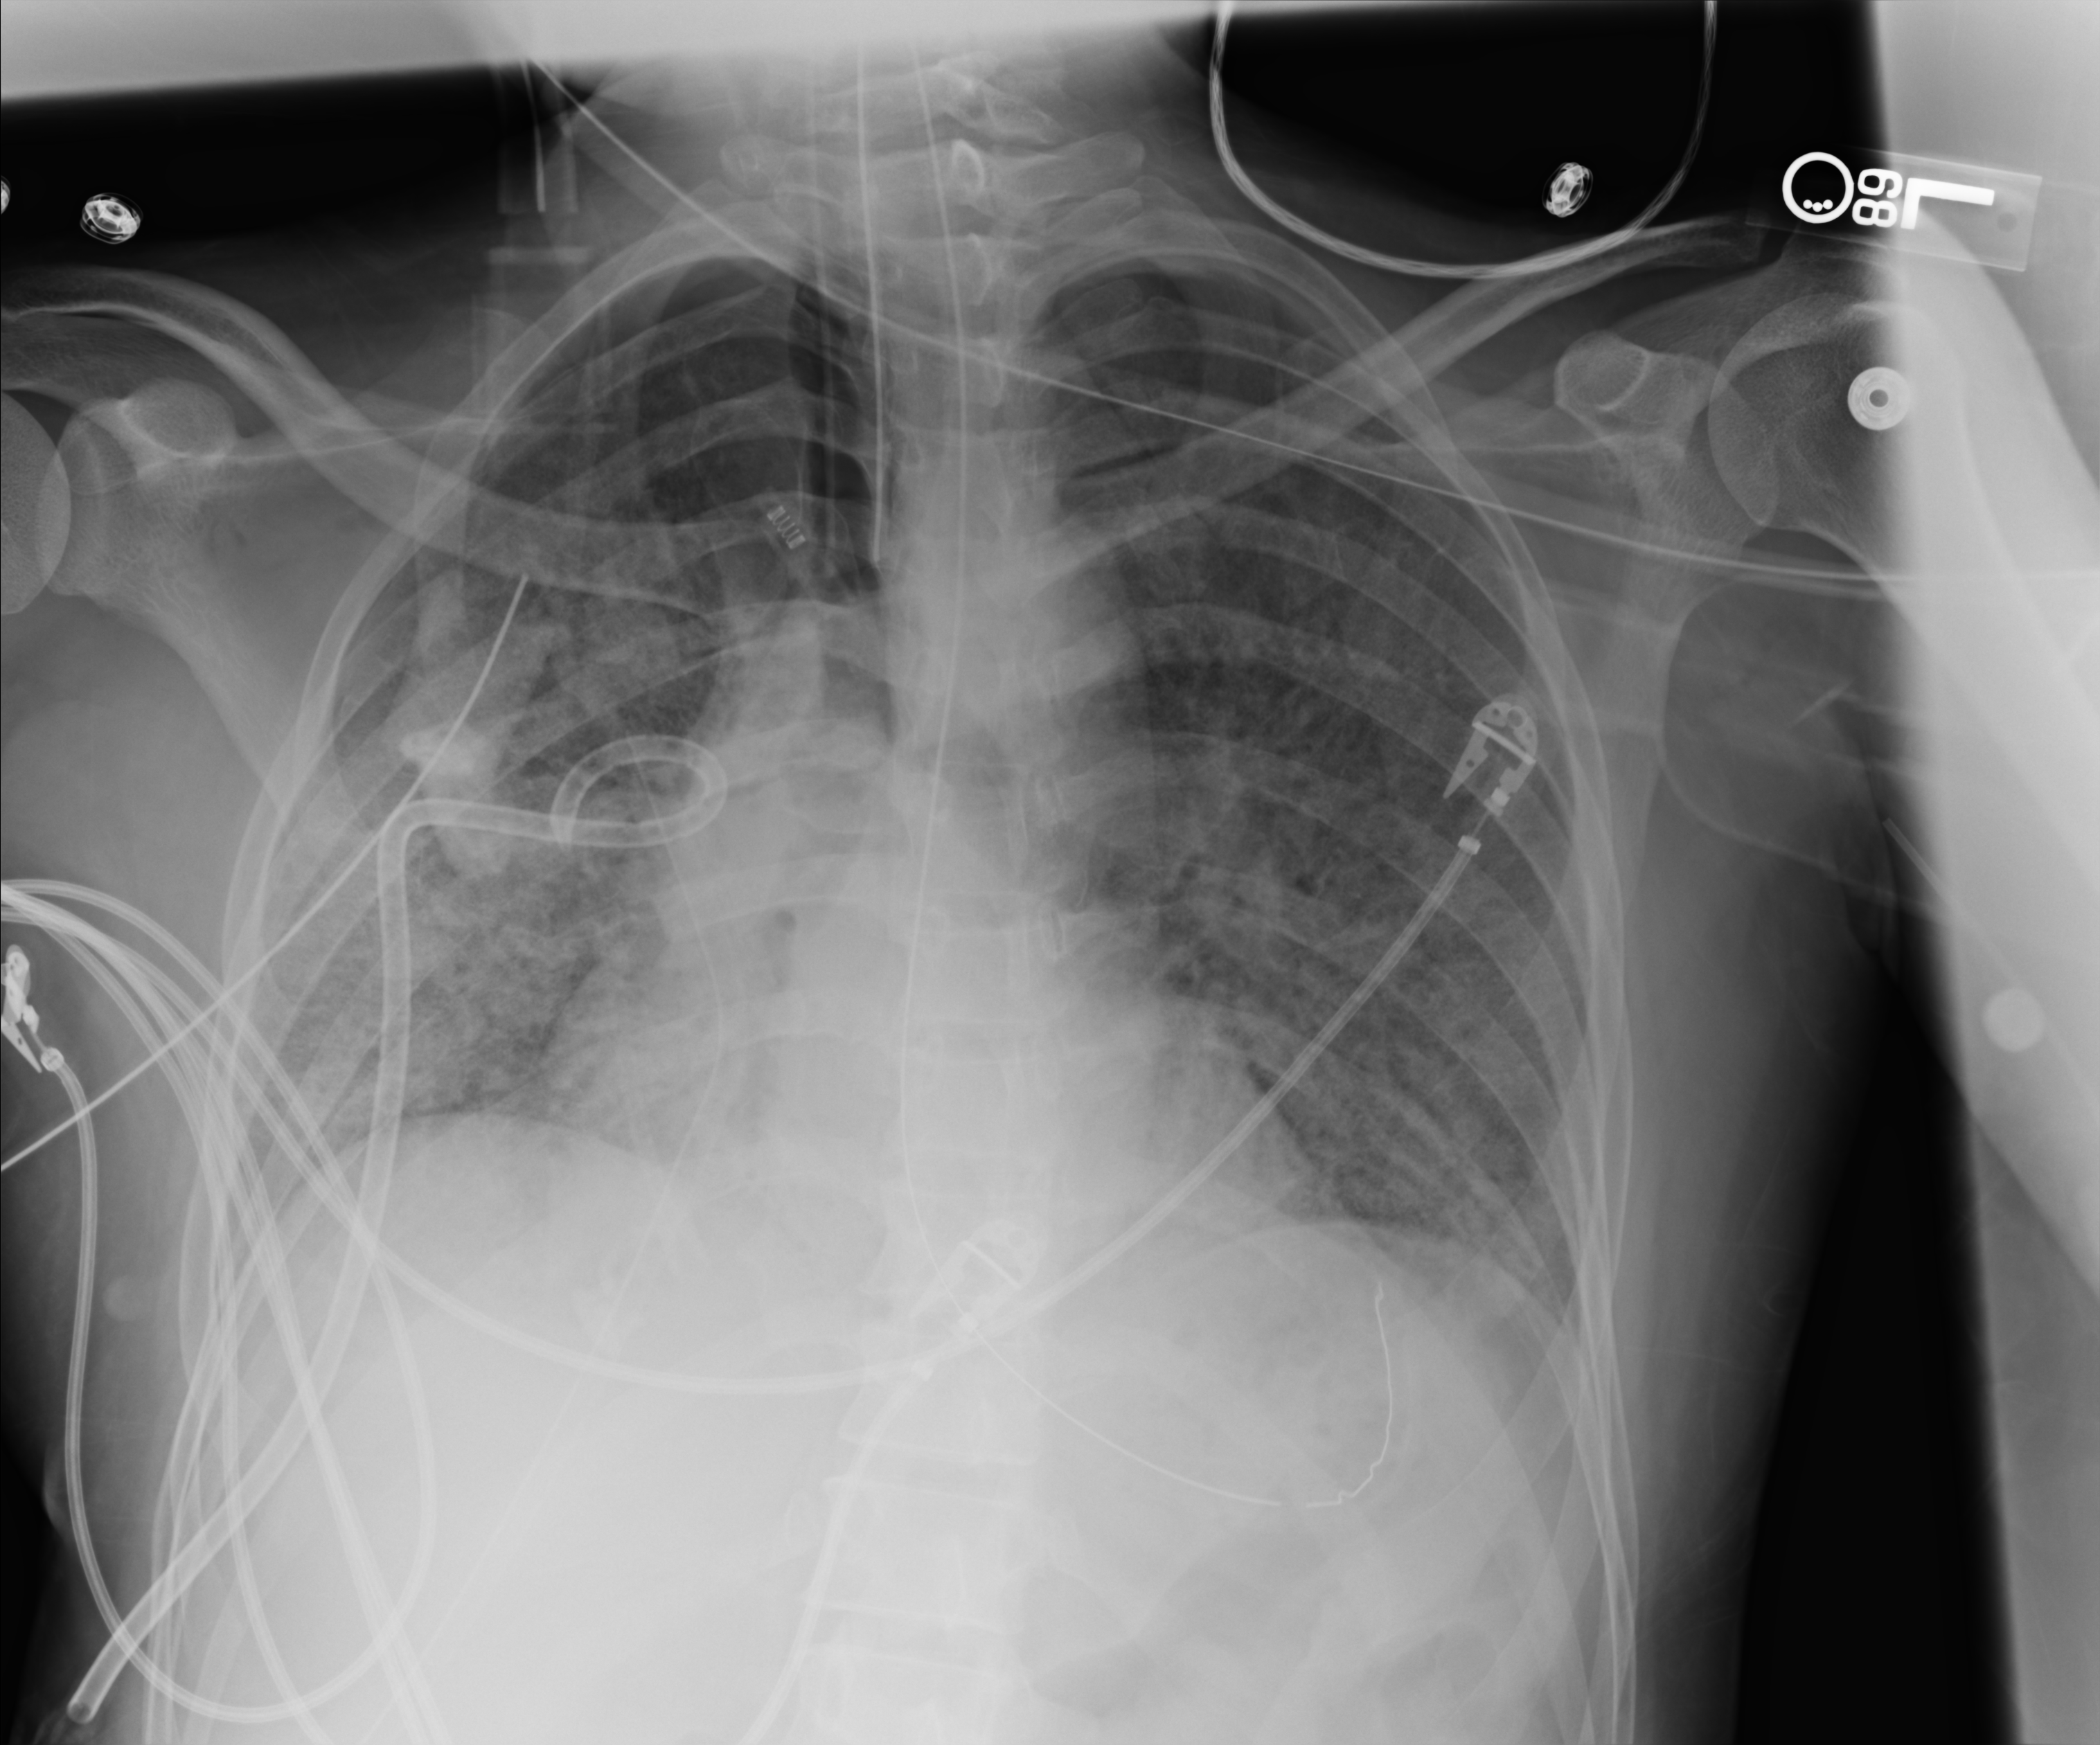
Chest X-ray (portable), anteroposterior (AP) projection. Adult patient hospitalised with COVID-19, age 18–59 years.
Admission-level facts for this patient (not findings on this image; timing relative to this image not recorded):
- diabetes (admission record): no
- chronic kidney disease (admission record): no
- mechanically ventilated during this hospital stay: yes